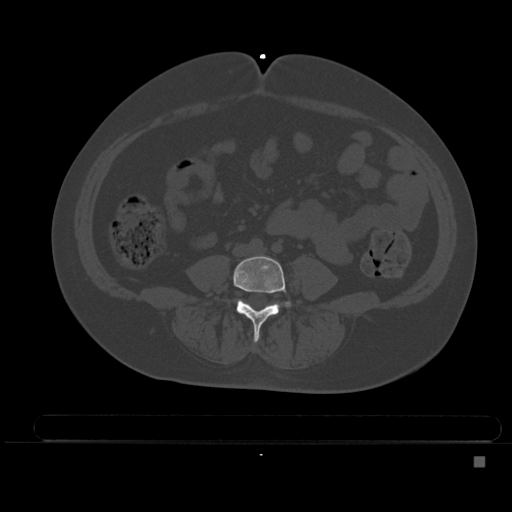
CT including the spine, one axial slice. Slice 127 of 495 in the series (ordered by position). Bone window (W 1800 / L 400 HU). 512 × 512 image matrix, field of view 404 × 404 mm. Female patient, age 33 years. From the clinical record (not read from this slice): primary cancer: breast; vertebrae with lytic lesions (as recorded): T1.
Annotated regions visible in this slice (semi-automatically segmented with operator editing):
- L4 vertebra: box from (x=233, y=255) to (x=292, y=341) px